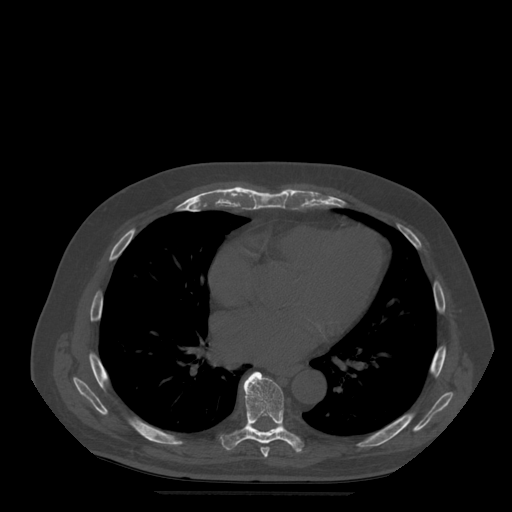
CT including the spine, one axial slice; bone window (W 1800 / L 400 HU); 1.25 mm slice thickness; 512 × 512 image matrix, field of view 420 × 420 mm. Patient age 72 years. Case-level facts recorded for this patient, not image findings: primary cancer: prostate.
Outlined on this slice (semi-automatically segmented with operator editing):
- T7 vertebra: box from (x=260, y=448) to (x=270, y=458) px
- T8 vertebra: (x=221, y=372)–(x=303, y=453)